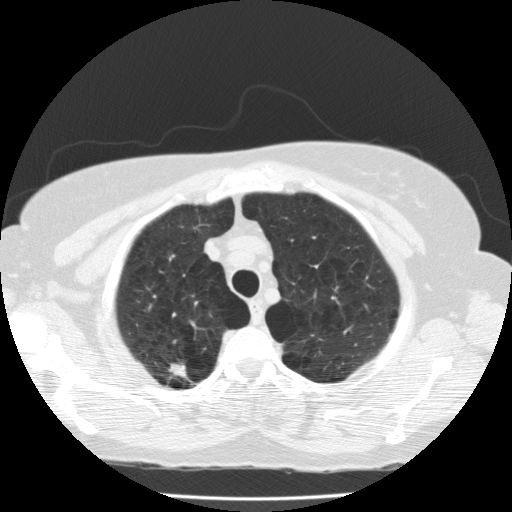
Axial slice from a low-dose chest CT screening exam. Second annual screen. Lung window (W 1500 / L -600 HU). 2 mm slice thickness. Standard (soft-tissue) reconstruction kernel (FC10). Slice 28 of 174 in the series. 512 × 512 image matrix. Female, age 59 years at enrolment.
Expert reader's lesion annotation, box from (x=145, y=352) to (x=203, y=396) px. The exam's reader record, not a measurement of the box and not confirmed to be the same lesion: non-calcified nodule or mass ≥4 mm, right upper lobe, 11 × 6 mm, spiculated (stellate) margins, soft tissue attenuation, pre-existing on the prior screen: yes; interval growth: no. Official screen result: positive, no significant change: stable abnormalities potentially related to lung cancer, unchanged since the prior screening exam.